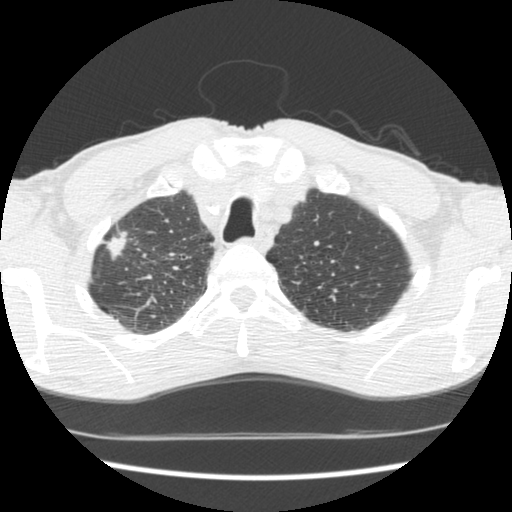
Low-dose screening chest CT, axial slice; baseline screening round; lung window (W 1500 / L -600 HU); 2.5 mm slice thickness. Male, age 62 years at enrolment. Current smoker at enrolment.
• Lesion marked by an expert reader, box from (x=87, y=222) to (x=139, y=273) px.
• Screening reader's record for this exam: no non-calcified nodule ≥4 mm recorded.
• Official screen result: negative screen, significant abnormalities not suspicious for lung cancer.
• Participant outcome: lung cancer diagnosed 640 days after this screen — adenocarcinoma, NOS, right upper lobe, poorly differentiated (G3), stage IIA (AJCC 6th edition), 22 mm at pathology.